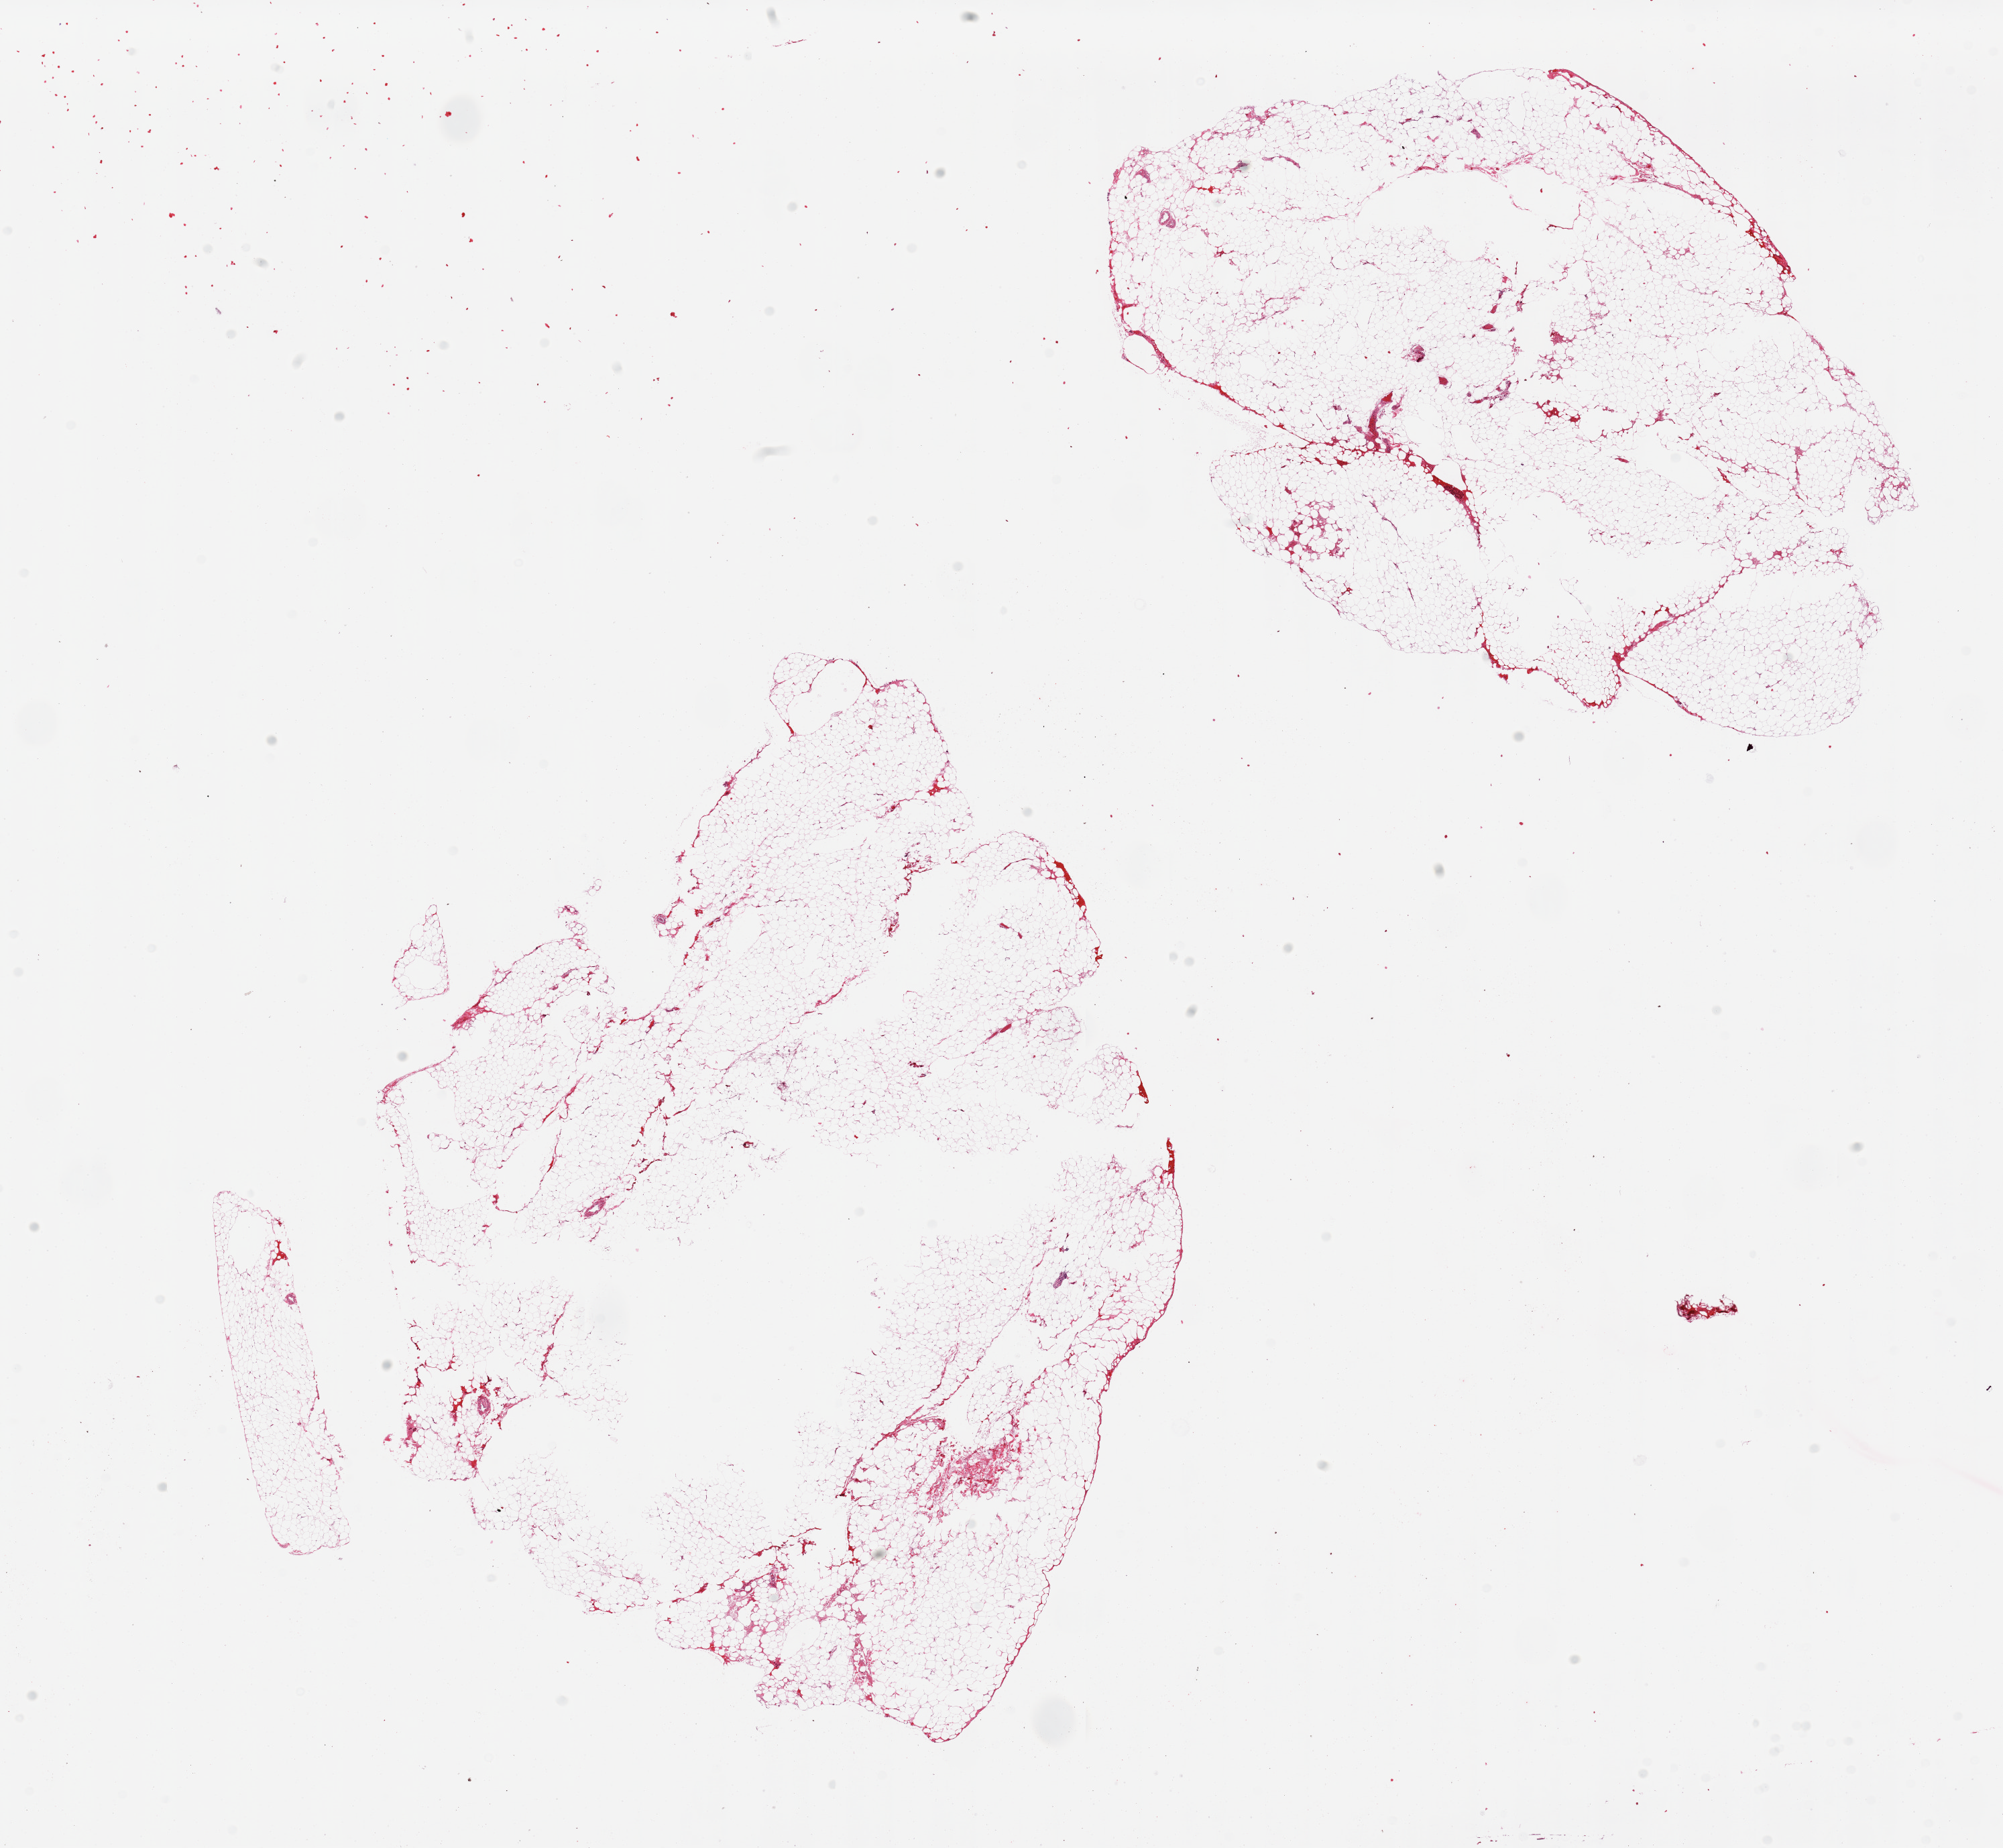
Hematoxylin and eosin (H&E) whole-slide image — low-resolution overview of the scanned area, about 23.6 x 21.8 mm. PAXgene-fixed paraffin-embedded (PFPE) section. Sampled site (target tissue): omentum. Donor tissue sample. Donor: male.
Reviewer comment on this tissue sample: 2 pieces; central holes.